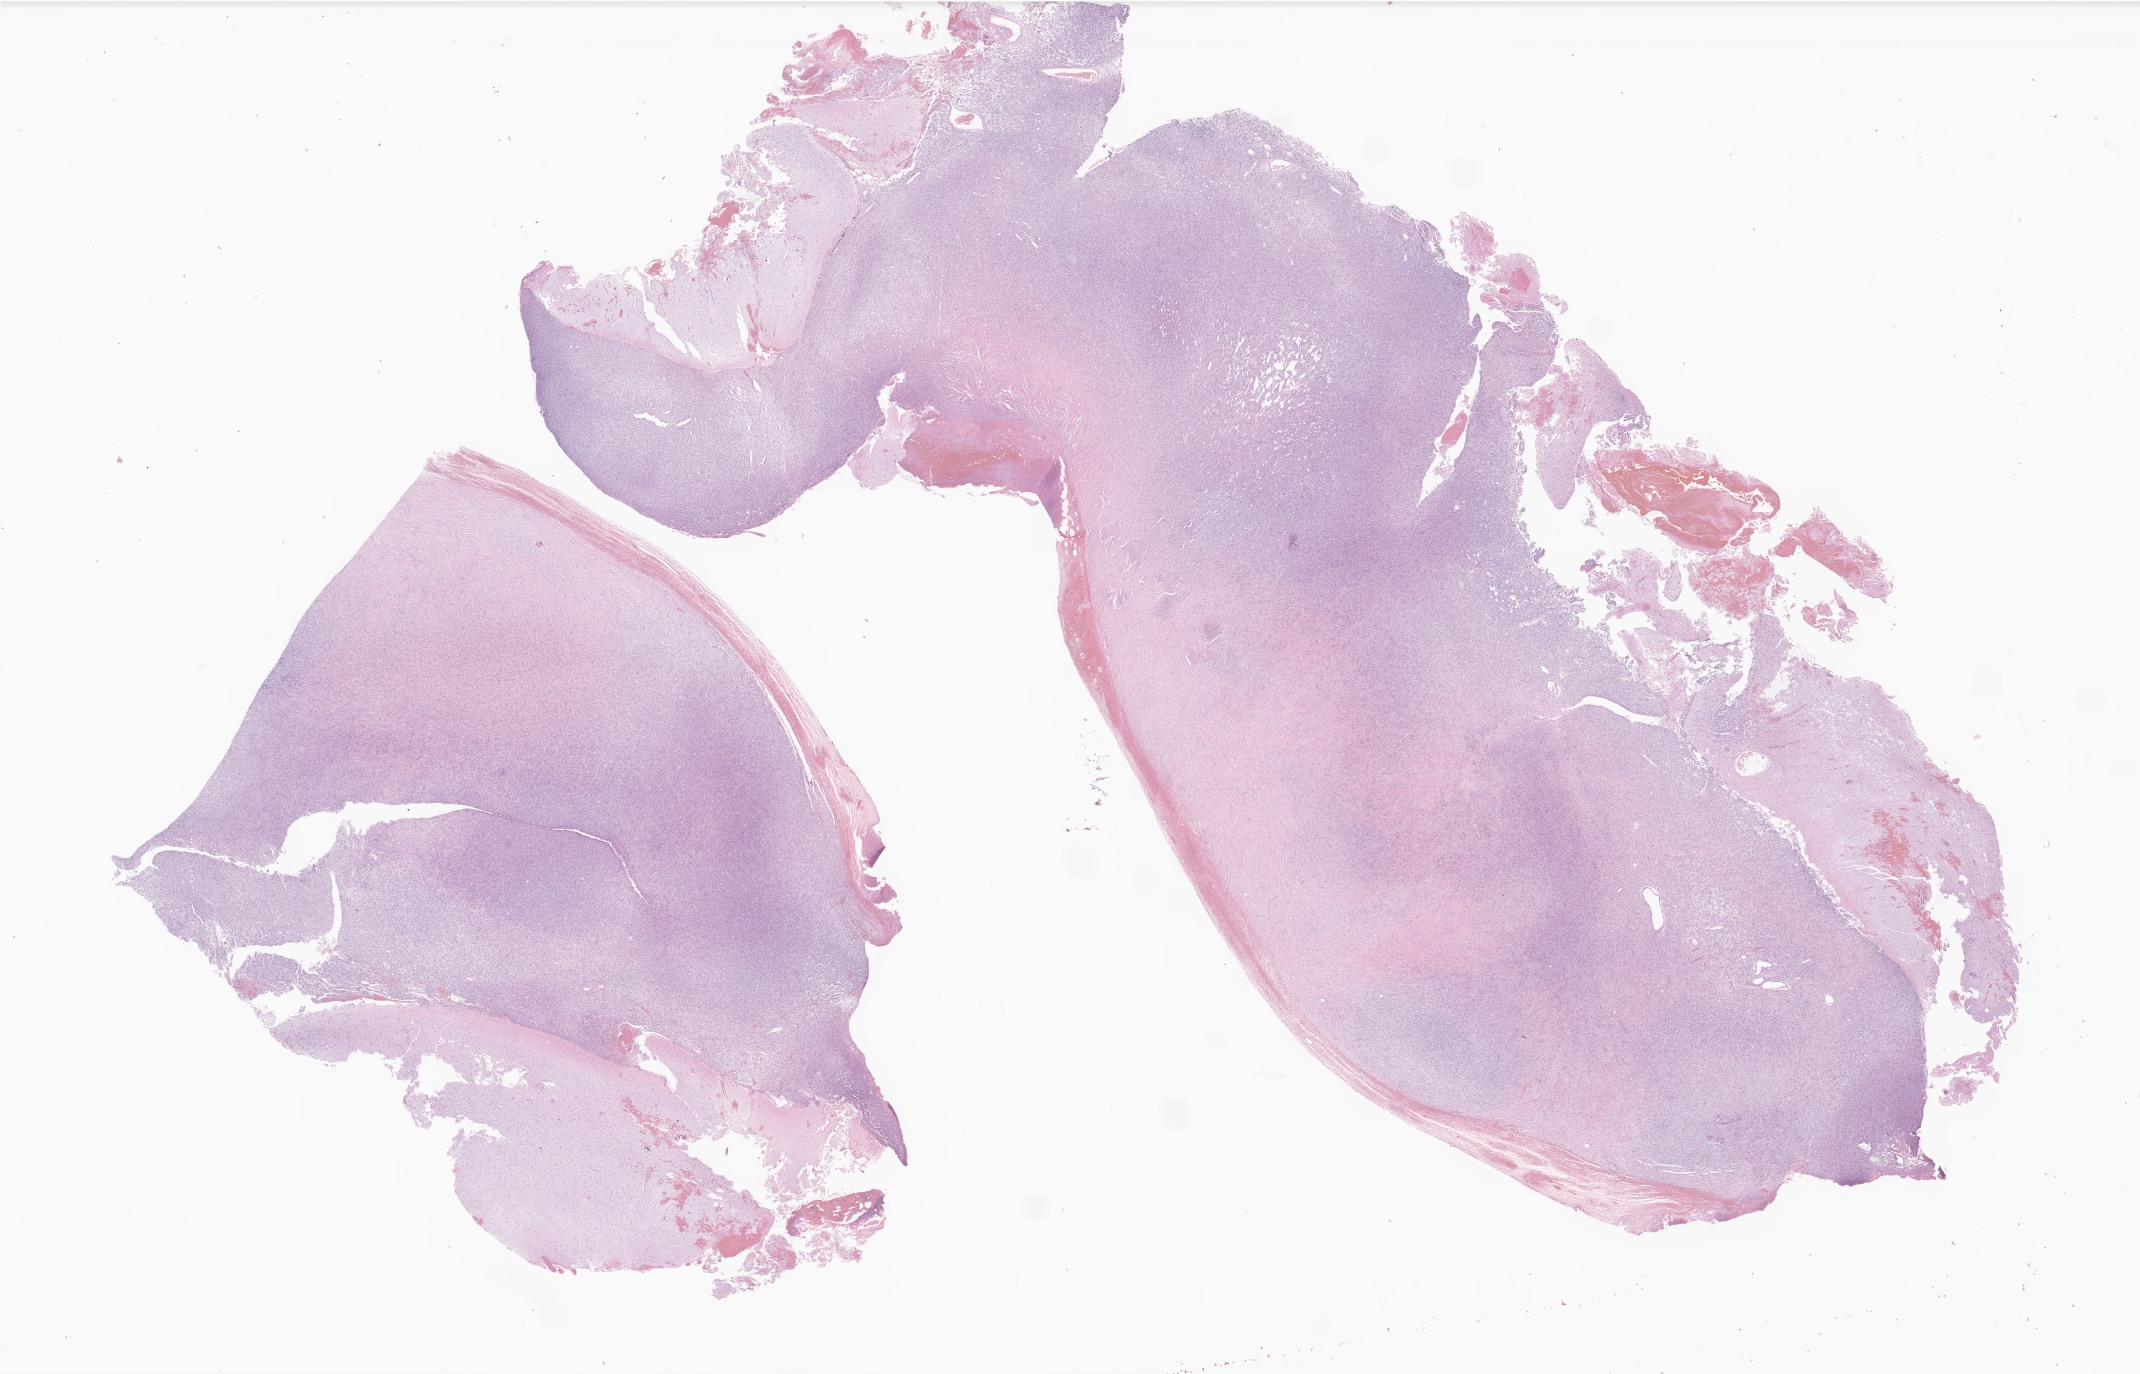
Whole-slide image, H&E stain of tumor tissue from the brain, whole scanned area (about 36.1 x 23.2 mm) shown as a low-resolution overview; formalin-fixed, paraffin-embedded (FFPE) tissue. Patient female; age 421 days (about 1.2 years).
* recorded diagnosis: Neoplasm, uncertain whether benign or malignant